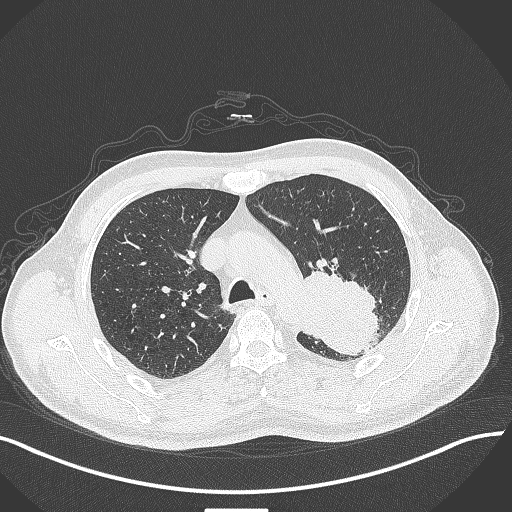
Chest CT, one axial slice. Slice 305 of 429 in the series (ordered by position). Reconstruction kernel B70f. Lung window (W 1500 / L -600 HU). 512 × 512 image matrix, field of view 400 × 400 mm. Male patient, age 55 years. Case-level facts recorded for this patient, not image findings: clinical TNM (as recorded): T3 N0 M1c.
Outlined on this slice (rectangle marked by the reading radiologist):
- lung tumour (recorded histology: adenocarcinoma): box from (x=292, y=266) to (x=384, y=357) px